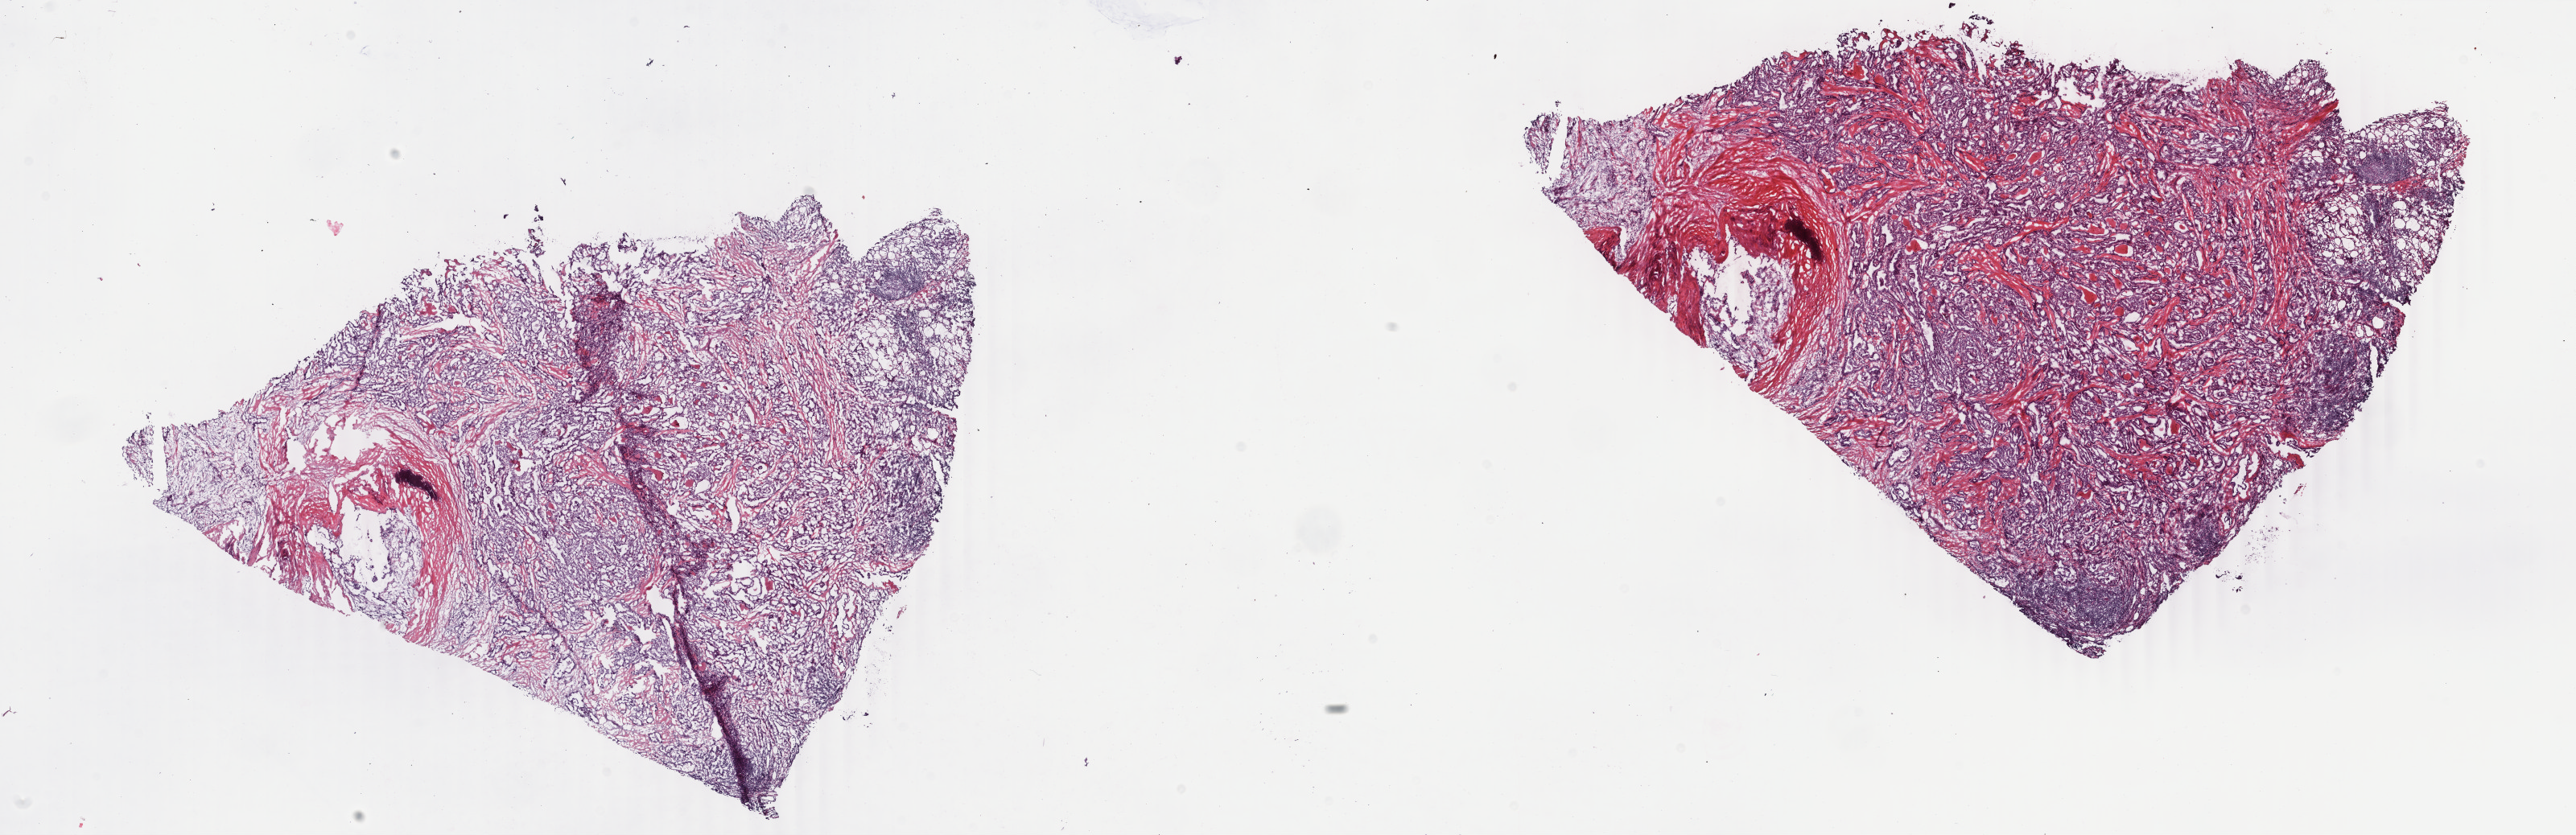
Hematoxylin and eosin (H&E) stained whole-slide image — low-resolution overview of the scanned area, about 25.5 x 8.3 mm (from a 40x scan), frozen section from the top of the tissue portion, primary tumour sample from the thyroid. Male, age 47 years at initial diagnosis. Pathologist review of this section (percent, as recorded): tumour cells 50%, tumour nuclei 90%, normal cells 10%, stromal cells 40%, necrosis 0%. Infiltration values recorded for this section: lymphocyte infiltration 20%, monocyte infiltration 4%, neutrophil infiltration 0%.
* diagnosis: Papillary adenocarcinoma, NOS (thyroid gland)
* AJCC pathologic stage: III (7th edition)
* lymph nodes positive (case pathology): 6 of 14 examined